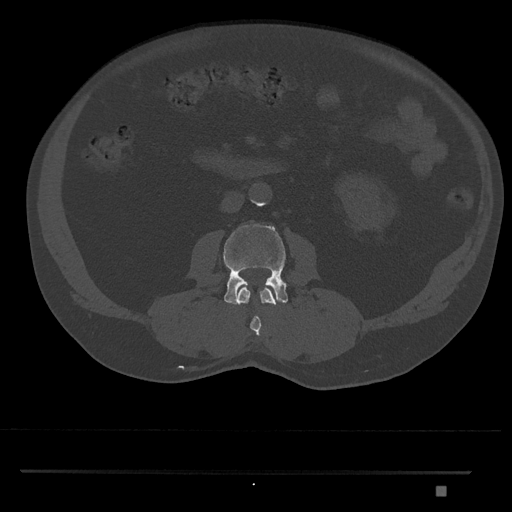
CT including the spine, one axial slice; slice 707 of 1134 in the series (ordered by position); 120 kVp; bone window (W 1800 / L 400 HU); 0.5 mm slice thickness; 512 × 512 image matrix, field of view 429 × 429 mm. Male patient, age 65 years. From the clinical record (not read from this slice): primary cancer: prostate.
Structures marked on this image (semi-automatically segmented with operator editing):
- L2 vertebra: box from (x=238, y=286) to (x=276, y=336) px
- L3 vertebra: (x=223, y=224)–(x=288, y=305)